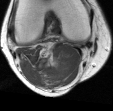
MRI of an extremity soft-tissue mass, one axial slice; position 12 of 45 along the scan axis; MR volume resampled by the dataset authors to the PET/CT grid (not the native acquisition matrix); 113 × 111 image matrix. Female patient. Case-level facts recorded for this patient, not image findings: histological type: liposarcoma; site of the primary tumour: right thigh.
Annotated regions visible in this slice (expert contour drawn on MRI and transferred to this co-registered scan by the dataset authors):
- gross tumour volume (mass): bounding box [x1, y1, x2, y2] px = [42, 65, 63, 84]